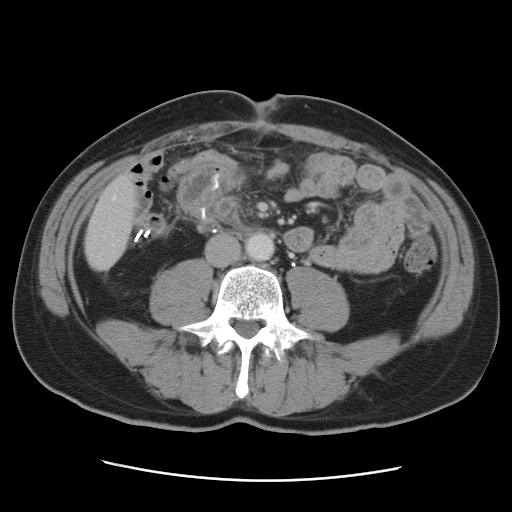
Contrast-enhanced abdominal CT, one axial slice; position 10 of 89 along the scan axis; 120 kVp; intravenous contrast given; soft-tissue window (W 400 / L 40 HU); 5 mm slice thickness; 512 × 512 image matrix, field of view 366 × 366 mm. Male patient, age 59 years. Case-level facts recorded for this patient, not image findings: diagnosis: colorectal cancer liver metastases, imaged before liver resection; multiple liver metastases: yes; largest metastasis: 0.6 cm; disease in both lobes: yes.
Outlined on this slice (expert manual segmentation):
- hepatic veins: bounding box [x1, y1, x2, y2] px = [113, 197, 115, 200]
- liver: [85, 177, 138, 269]
- planned liver remnant (the part of the liver to remain after resection): [85, 177, 138, 258]